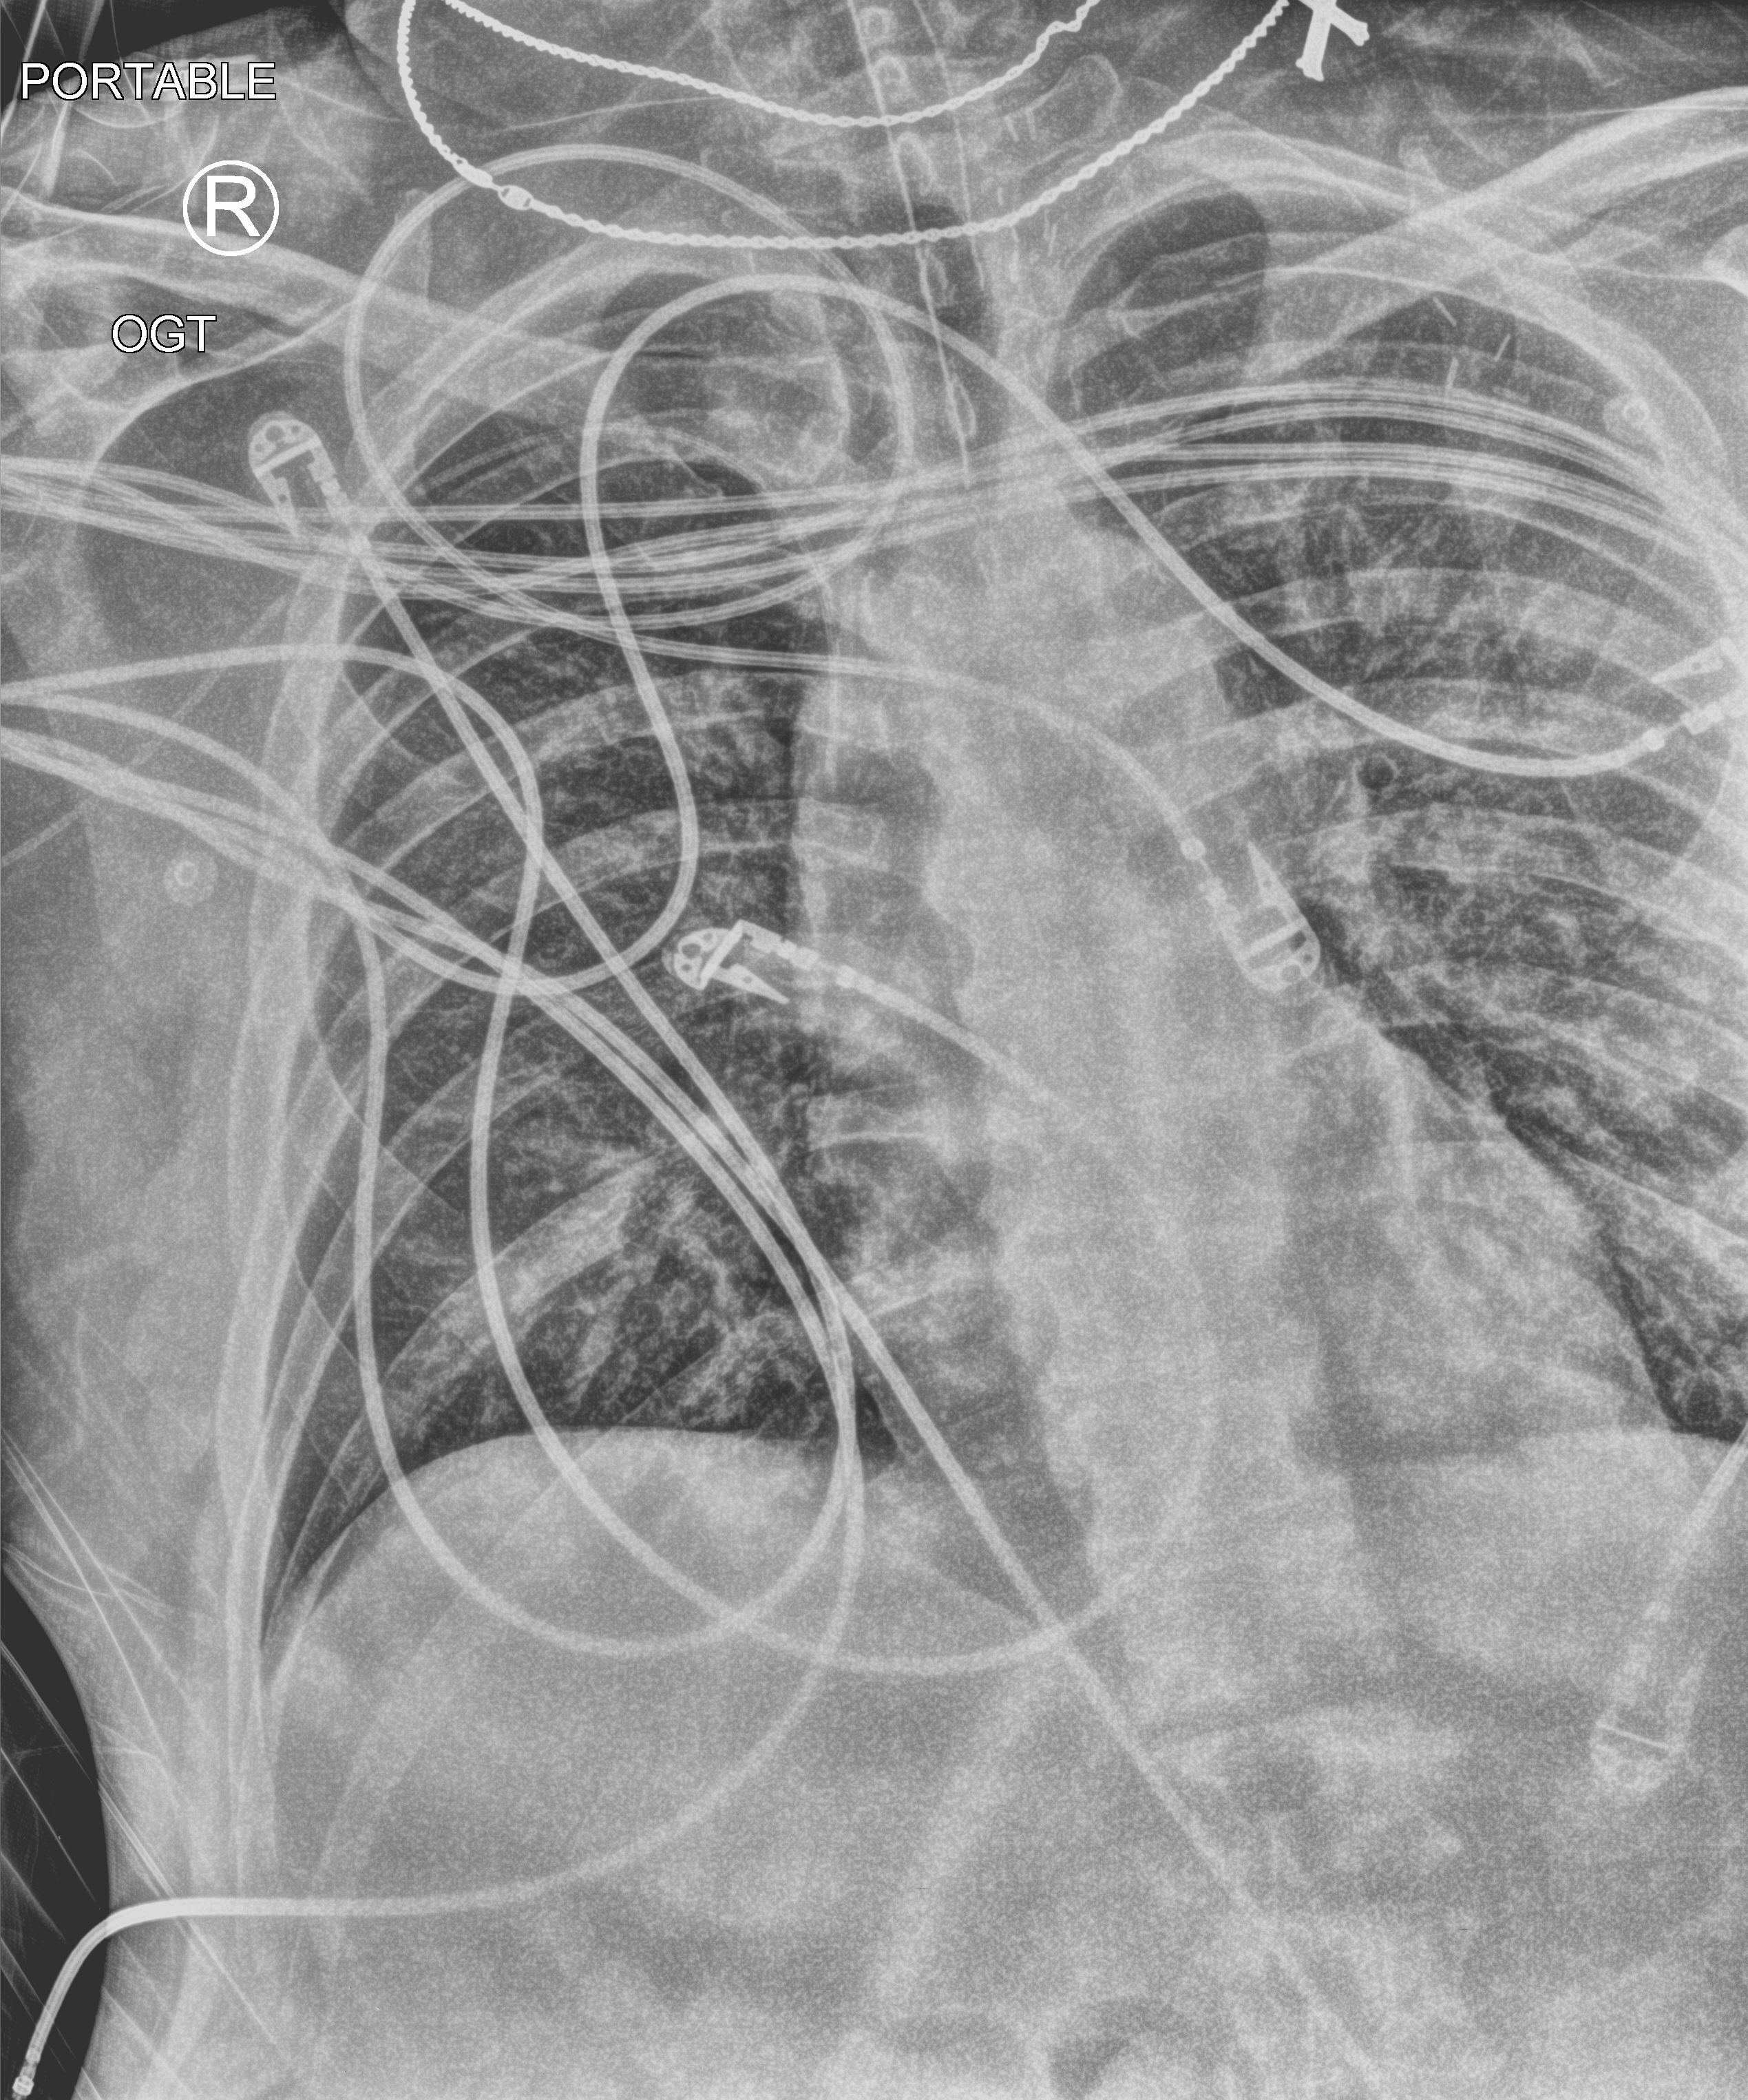
Portable chest radiograph, anteroposterior (AP) projection. Adult patient hospitalised with COVID-19, age 18–59 years.
Admission-level facts for this patient (not findings on this image; timing relative to this image not recorded): mechanically ventilated during this hospital stay: yes; admitted to intensive care during this hospital stay: yes.